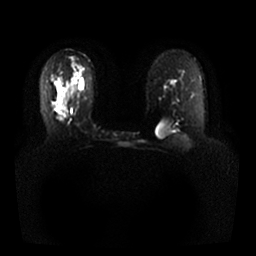
Breast MRI, one axial slice. Slice 17 of 25 in the series (ordered by position). Diffusion-weighted series; image 2 of 4 stored at this slice position (different b-values; order by instance number). 1.5 T. 4 mm slice thickness. 256 × 256 image matrix. Female patient.
Outlined on this slice (outlined manually by an expert reader):
- tumour on diffusion-weighted imaging: bounding box (x1, y1, x2, y2) in pixels: (57, 104, 63, 115)